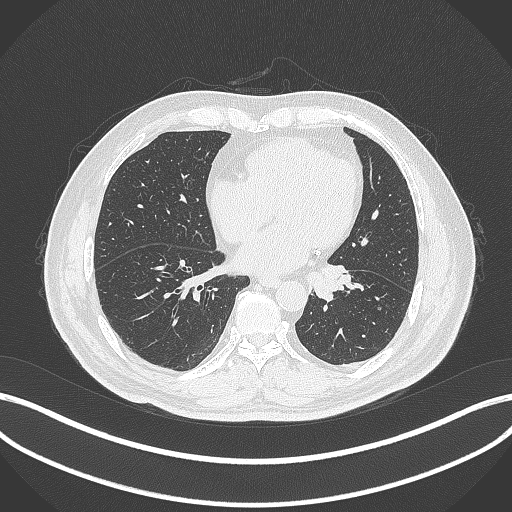
Chest CT, one axial slice; position 103 of 312 along the scan axis; 120 kVp; lung window (W 1500 / L -600 HU); 1 mm slice thickness; 512 × 512 image matrix, field of view 400 × 400 mm. Male patient, age 71 years. Case-level facts recorded for this patient, not image findings: clinical TNM (as recorded): T1b N0 M0.
Annotated regions visible in this slice (rectangle marked by the reading radiologist):
- lung tumour (recorded histology: squamous cell carcinoma): bounding box [x1, y1, x2, y2] px = [304, 262, 354, 301]